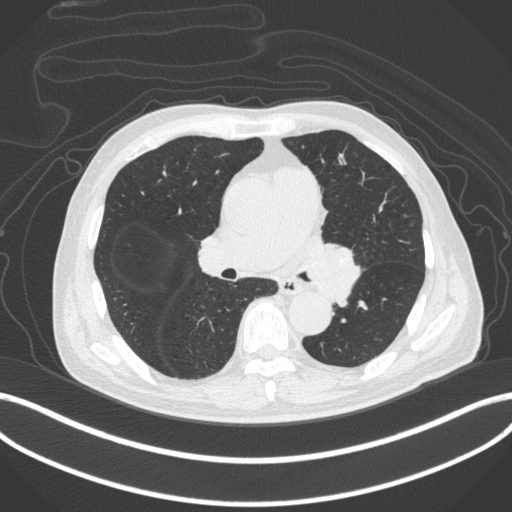
Chest CT, one axial slice; slice 240 of 420 in the series (ordered by position); lung window (W 1500 / L -600 HU); 512 × 512 image matrix, field of view 400 × 400 mm. Male patient, age 77 years. From the clinical record (not read from this slice): clinical TNM (as recorded): T3 N1 M0.
Structures marked on this image (bounding box drawn by a radiologist):
- lung tumour (recorded histology: adenocarcinoma): box from (x=302, y=235) to (x=364, y=309) px